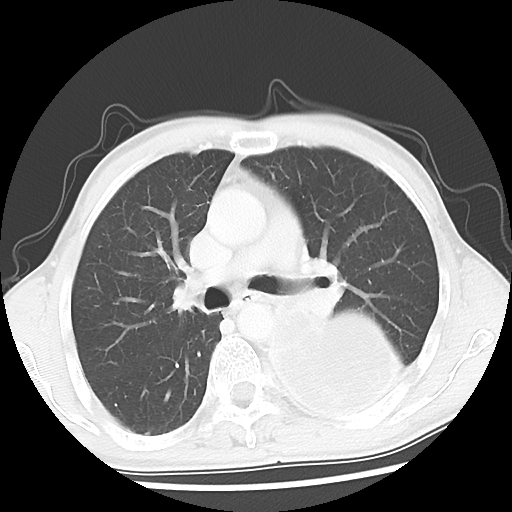
Chest CT, one axial slice. Position 31 of 52 along the scan axis. Reconstruction kernel LUNG. Lung window (W 1500 / L -600 HU). 512 × 512 image matrix, field of view 318 × 318 mm. Patient: male, 60 years. Case-level facts recorded for this patient, not image findings: clinical TNM (as recorded): T4 N0 M0.
Structures marked on this image (bounding box drawn by a radiologist):
- lung tumour (recorded histology: squamous cell carcinoma): bounding box <251,301,413,424> (left, top, right, bottom; pixels)